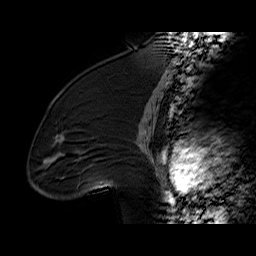
Breast MRI (dynamic contrast-enhanced), one sagittal slice; position 38 of 60 along the scan axis; dynamic contrast-enhanced series, time point 2 of 6 at this slice position (early post-contrast); 1.5 T; TE 6.2 ms, TR 32.4 ms; 4 mm slice thickness; 256 × 256 image matrix, field of view 200 × 200 mm. Female patient. Case-level facts recorded for this patient, not image findings: setting: breast cancer imaged before/during neoadjuvant chemotherapy; receptor status: triple-negative.
Structures marked on this image (semi-automatic segmentation, software-assisted and operator-edited):
- analysis volume of interest (the breast-tissue region the enhancement analysis was run in; not a lesion): bounding box (x1, y1, x2, y2) in pixels: (36, 97, 134, 196)
- tumour enhancement mask (voxels above the 100 % enhancement threshold inside the analysis volume of interest): (55, 136, 103, 184)